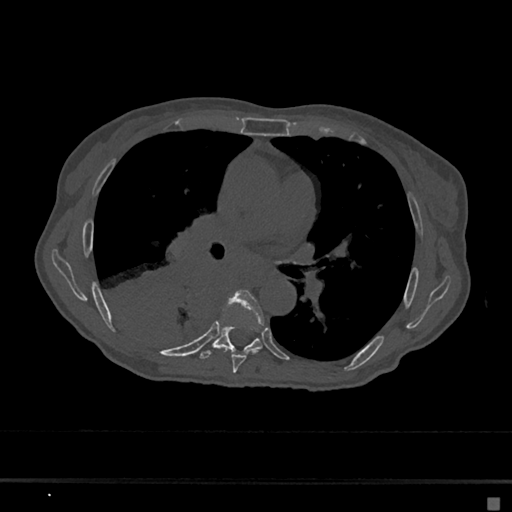
CT including the spine, one axial slice. Slice 396 of 797 in the series (ordered by position). 120 kVp. Bone window (W 1800 / L 400 HU). 0.5 mm slice thickness. 512 × 512 image matrix, field of view 360 × 360 mm. Patient: female, 68 years. Case-level facts recorded for this patient, not image findings: primary cancer: renal.
Structures marked on this image (semi-automatic segmentation, software-assisted and operator-edited):
- T6 vertebra: box from (x=228, y=290) to (x=264, y=373) px
- T7 vertebra: (x=200, y=327)–(x=263, y=359)